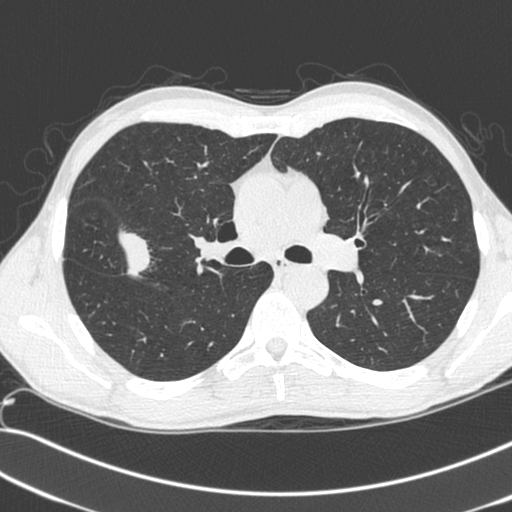
Axial slice from a low-dose chest CT screening exam; baseline annual screen; lung window (W 1500 / L -600 HU); 1.3 mm slice thickness; standard (soft-tissue) reconstruction kernel (C). Male participant, aged 55 years at enrolment. Current smoker at enrolment.
• Expert-annotated lung lesion, bounding box <66,216,158,295> (left, top, right, bottom; pixels).
• Reader record for this screening exam (exam-level; its link to the box is not recorded): non-calcified nodule or mass ≥4 mm, right upper lobe, 52 × 39 mm, spiculated (stellate) margins, soft tissue attenuation.
• Official screen result: positive, change unspecified: nodule(s) >= 4 mm or enlarging nodule(s), mass(es), or other non-specific abnormalities suspicious for lung cancer.
• Lung cancer was diagnosed 25 days after this screen: large cell neuroendocrine carcinoma, right upper lobe, poorly differentiated (G3), stage IIB (AJCC 6th edition), 49 mm at pathology.